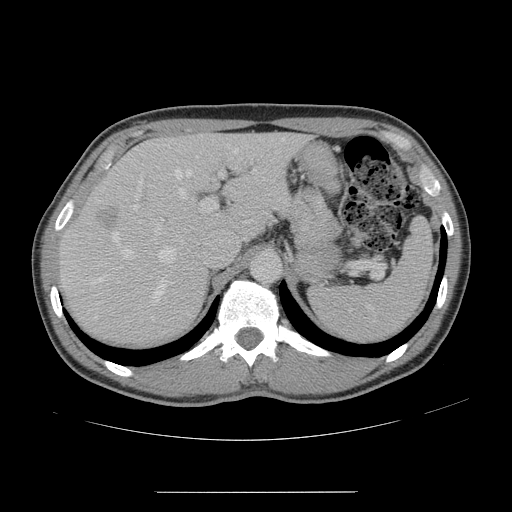
Contrast-enhanced abdominal CT, one axial slice. Slice 105 of 178 in the series (ordered by position). 120 kVp. Intravenous contrast given. Soft-tissue window (W 400 / L 40 HU). 2.5 mm slice thickness. 512 × 512 image matrix, field of view 401 × 401 mm. Male patient, age 53 years. Case-level facts recorded for this patient, not image findings: diagnosis: colorectal cancer liver metastases, imaged before liver resection; multiple liver metastases: yes; largest metastasis: 2.4 cm.
Annotated regions visible in this slice (manually delineated by an expert):
- hepatic veins: bounding box [x1, y1, x2, y2] px = [92, 139, 284, 306]
- liver: [62, 134, 303, 343]
- planned liver remnant (the part of the liver to remain after resection): [147, 135, 303, 237]
- portal vein (with intrahepatic branches): [133, 156, 224, 235]
- liver metastasis: [98, 208, 122, 230]